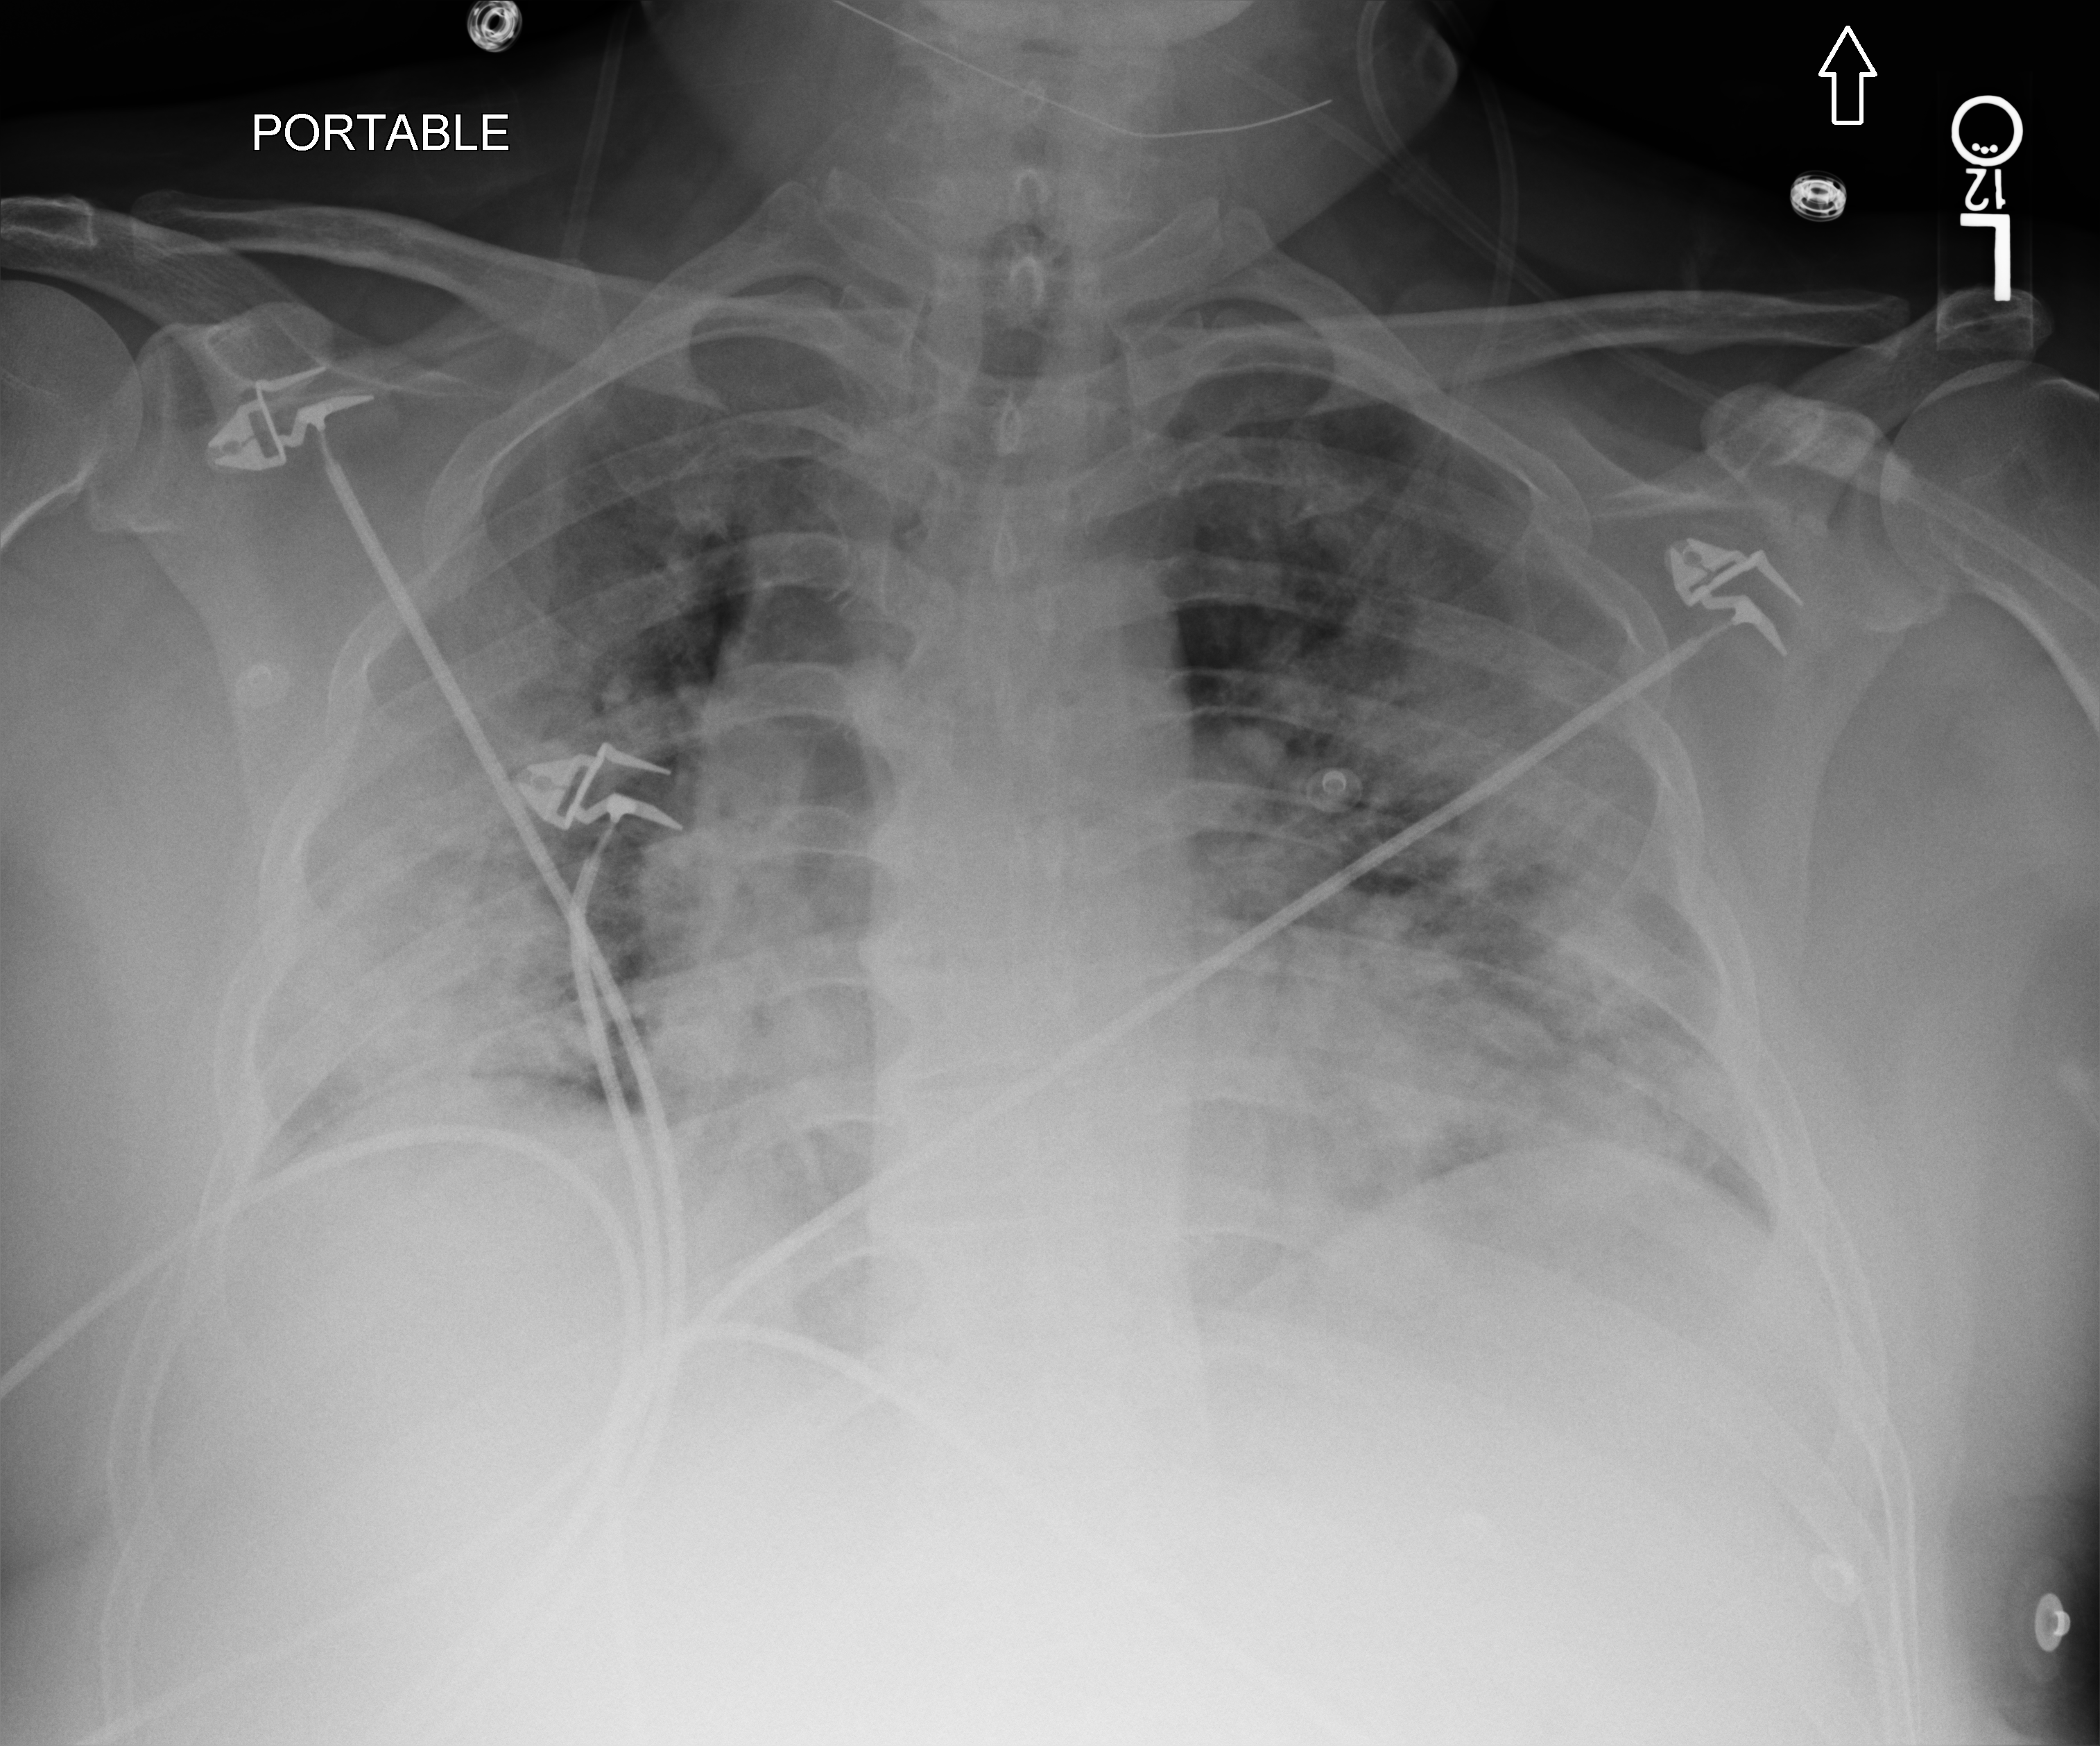
Bedside chest radiograph (computed radiography), anteroposterior (AP) projection. Patient hospitalised with COVID-19; male, aged 18–59 years.
Hospital-stay facts (about this admission, not read from this image; timing relative to this image not recorded): mechanically ventilated during this hospital stay: yes; other chronic lung disease (admission record): no; admitted to intensive care during this hospital stay: yes.